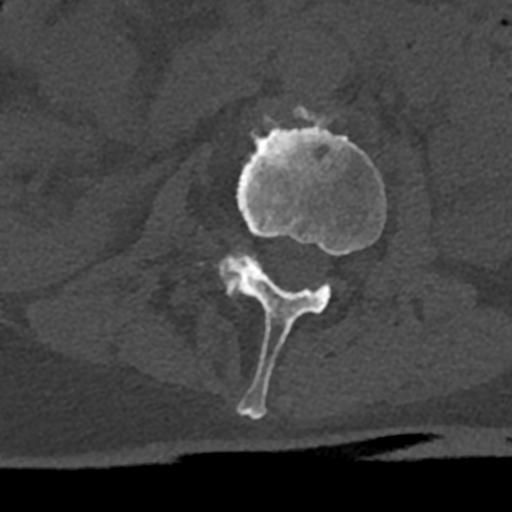
CT including the spine, one axial slice; slice 368 of 797 in the series (ordered by position); 120 kVp; bone window (W 1800 / L 400 HU); 512 × 512 image matrix. Male patient, age 74 years. Case-level facts recorded for this patient, not image findings: primary cancer: renal; vertebrae with lytic lesions (as recorded): T10, L1, L2, L3, L4, L5.
Outlined on this slice (semi-automatic segmentation, software-assisted and operator-edited):
- L2 vertebra: bounding box <218,105,386,419> (left, top, right, bottom; pixels)
- L3 vertebra: <222,251,254,296>